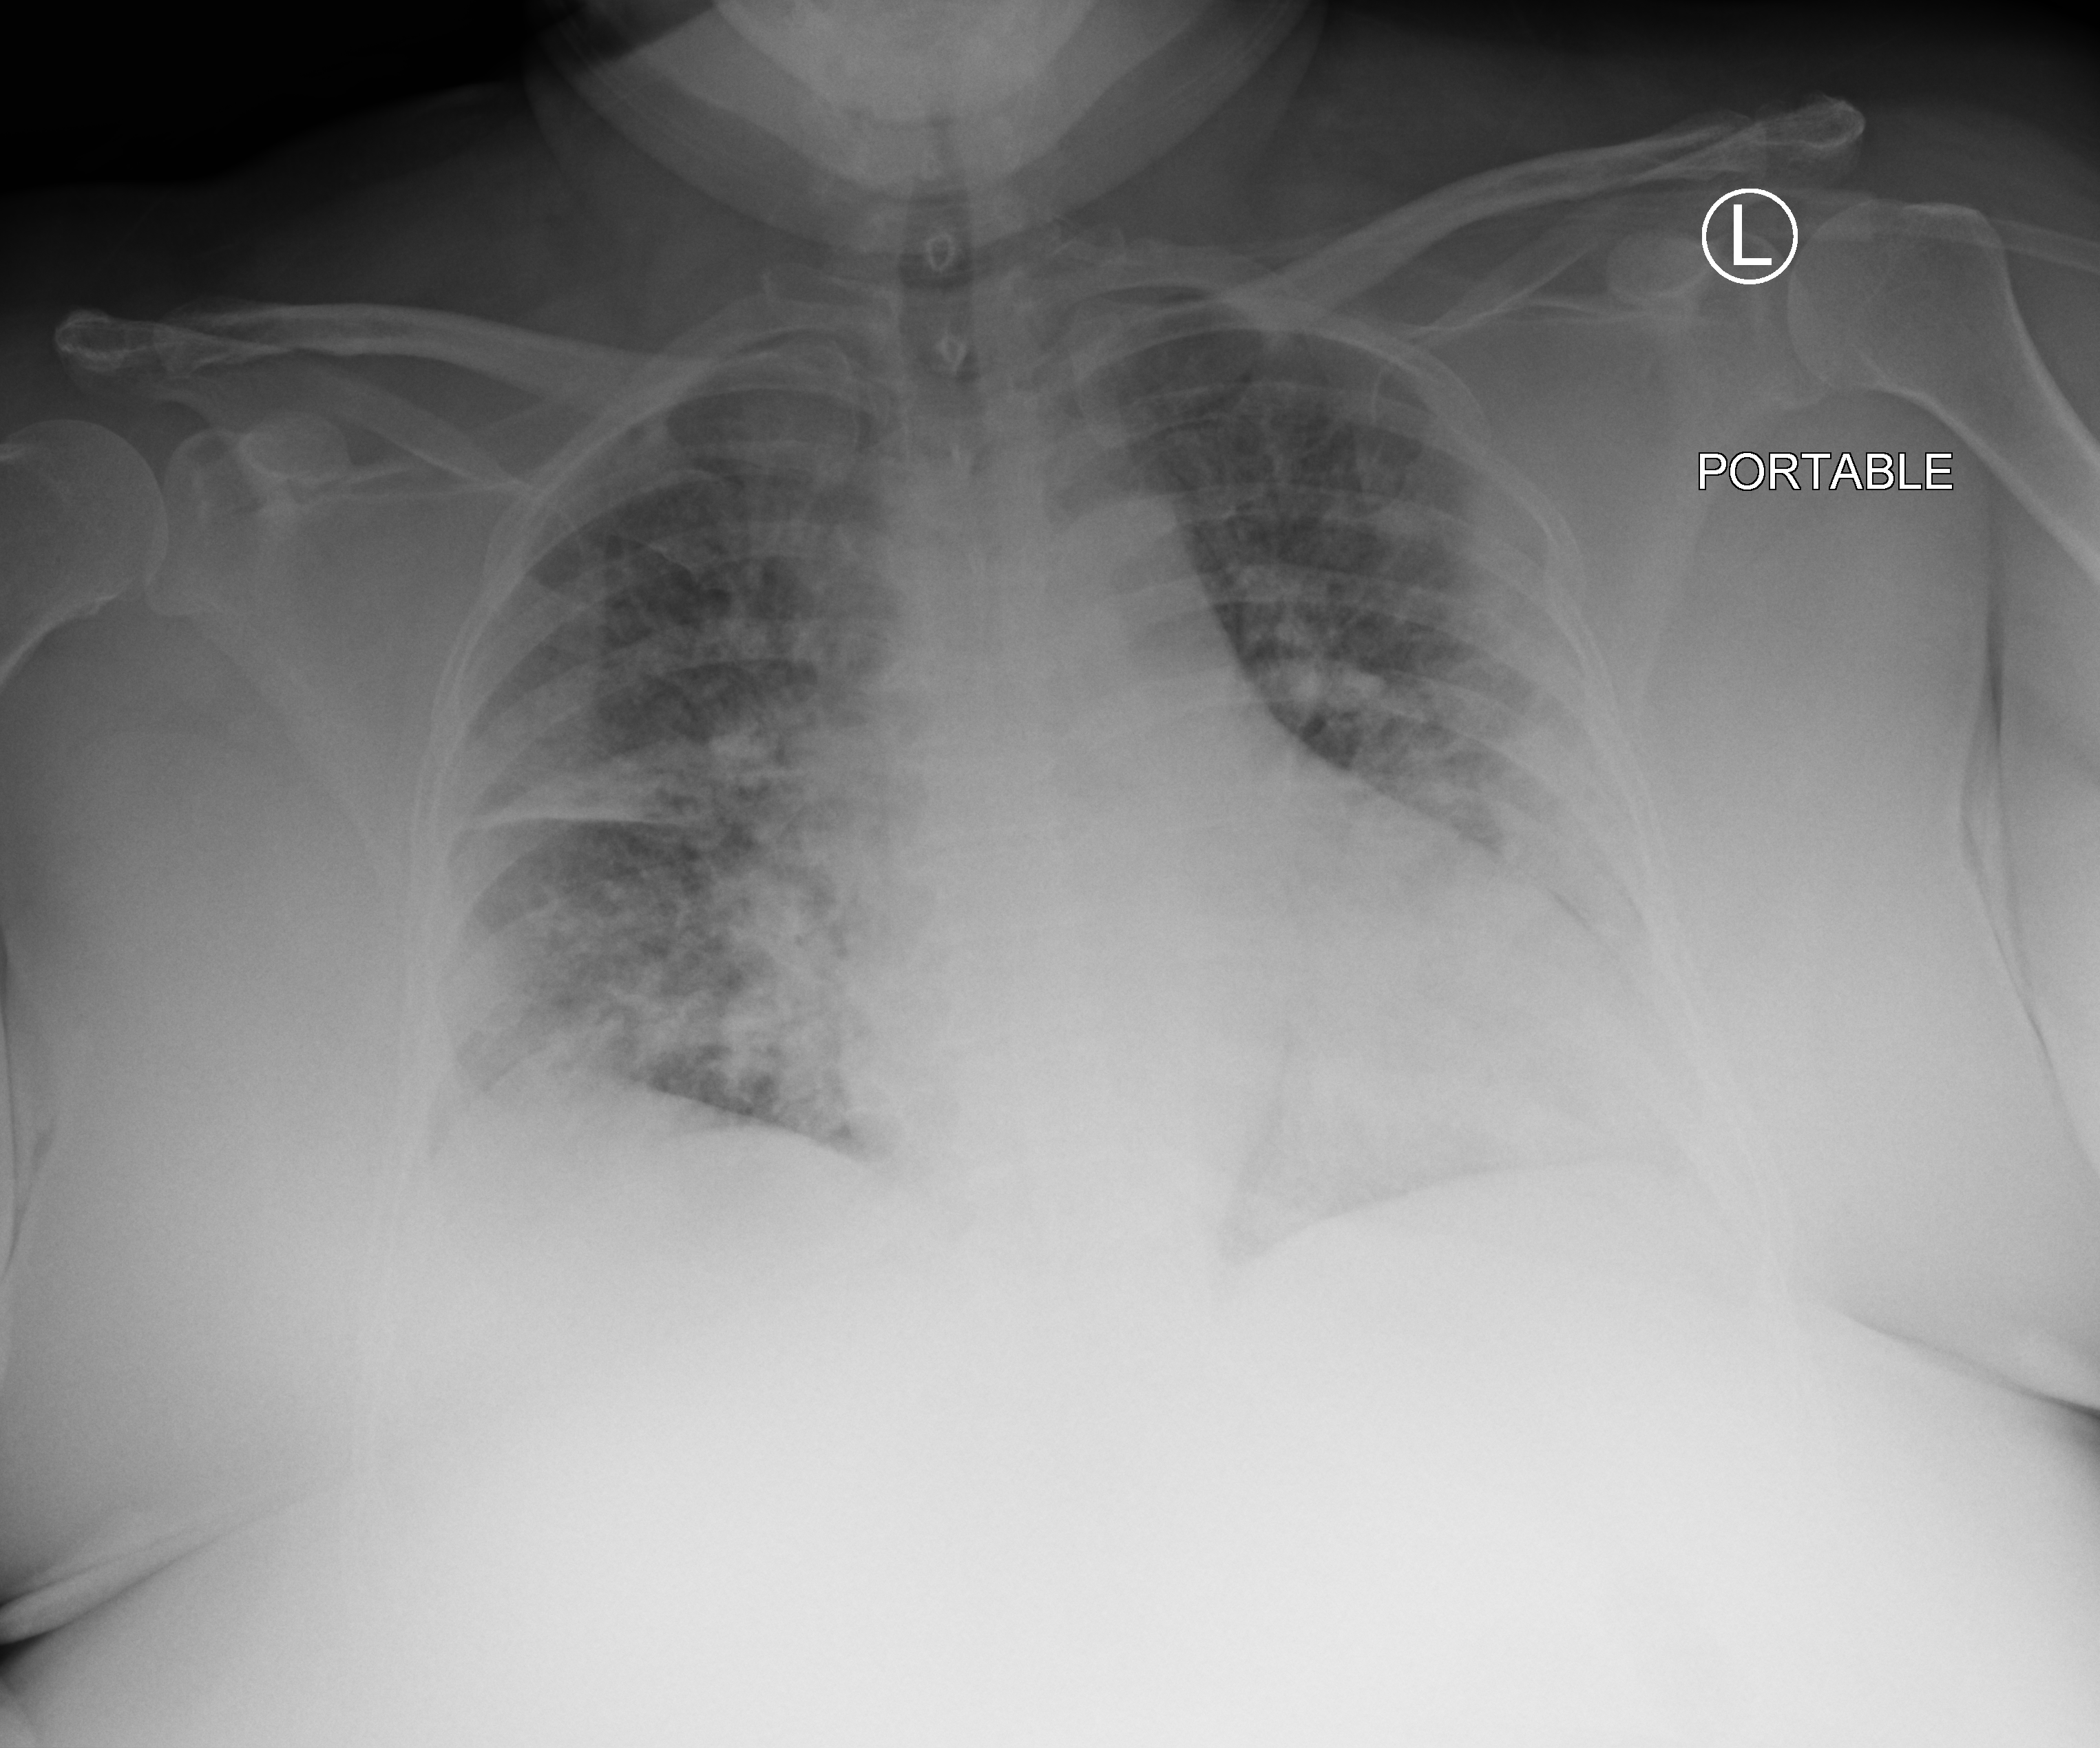
Chest X-ray (portable), anteroposterior (AP) projection. Female patient hospitalised with COVID-19, age 60–74 years.
Hospital-stay facts (about this admission, not read from this image; timing relative to this image not recorded):
- admitted to intensive care during this hospital stay: no
- length of hospital stay: 6 days
- COPD (admission record): no